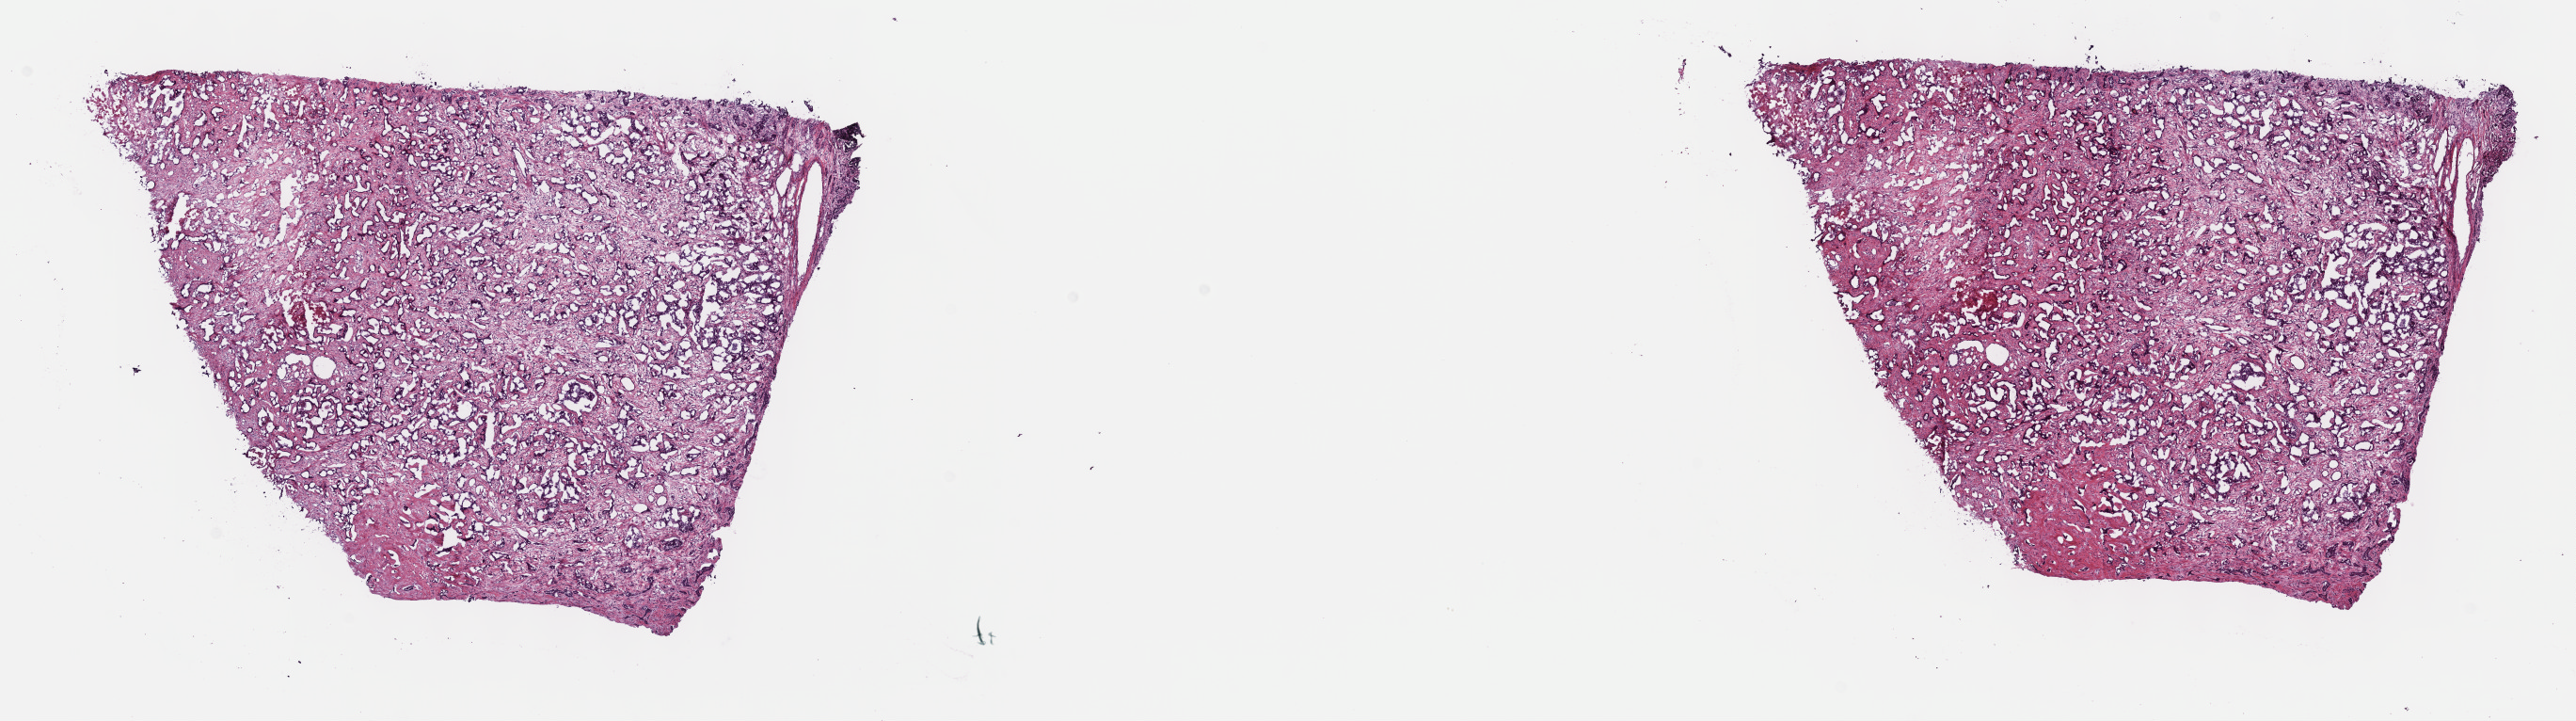
Digitized Hematoxylin and eosin (H&E) stained tissue section (whole slide) — shown as a low-resolution overview of the whole scanned area (about 22.1 x 6.2 mm, slide scanned at 40x), frozen section from the top of the tissue portion, bile duct, primary tumour sample. Patient: male, age at initial diagnosis 66 years. Histologic grade: G2 (moderately differentiated). Pathologist review of this section (percent, as recorded): tumour cells 75%, tumour nuclei 75%, normal cells 0%, stromal cells 25%, necrosis 0%. Infiltration values recorded for this section: lymphocyte infiltration 3%, monocyte infiltration 1%, neutrophil infiltration 3%.
* pathologic diagnosis: Cholangiocarcinoma (intrahepatic bile duct)
* AJCC pathologic stage: I (6th edition)